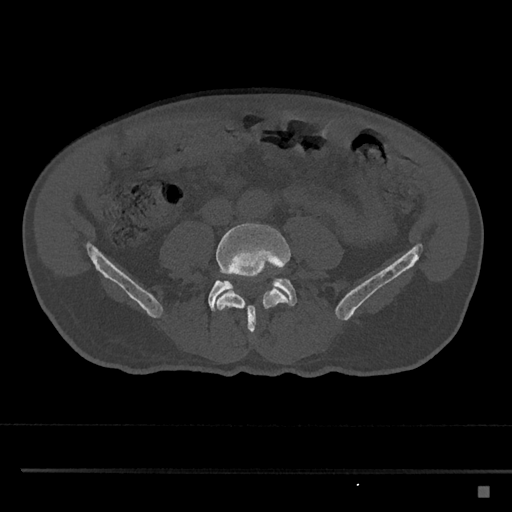
CT including the spine, one axial slice; reconstruction kernel Br40s/3; 120 kVp; bone window (W 1800 / L 400 HU); 512 × 512 image matrix, field of view 391 × 391 mm. Male patient, age 59 years. Case-level facts recorded for this patient, not image findings: primary cancer: prostate.
Outlined on this slice (semi-automatic segmentation, software-assisted and operator-edited):
- L4 vertebra: bounding box <215,223,291,333> (left, top, right, bottom; pixels)
- L5 vertebra: <208,278,298,311>